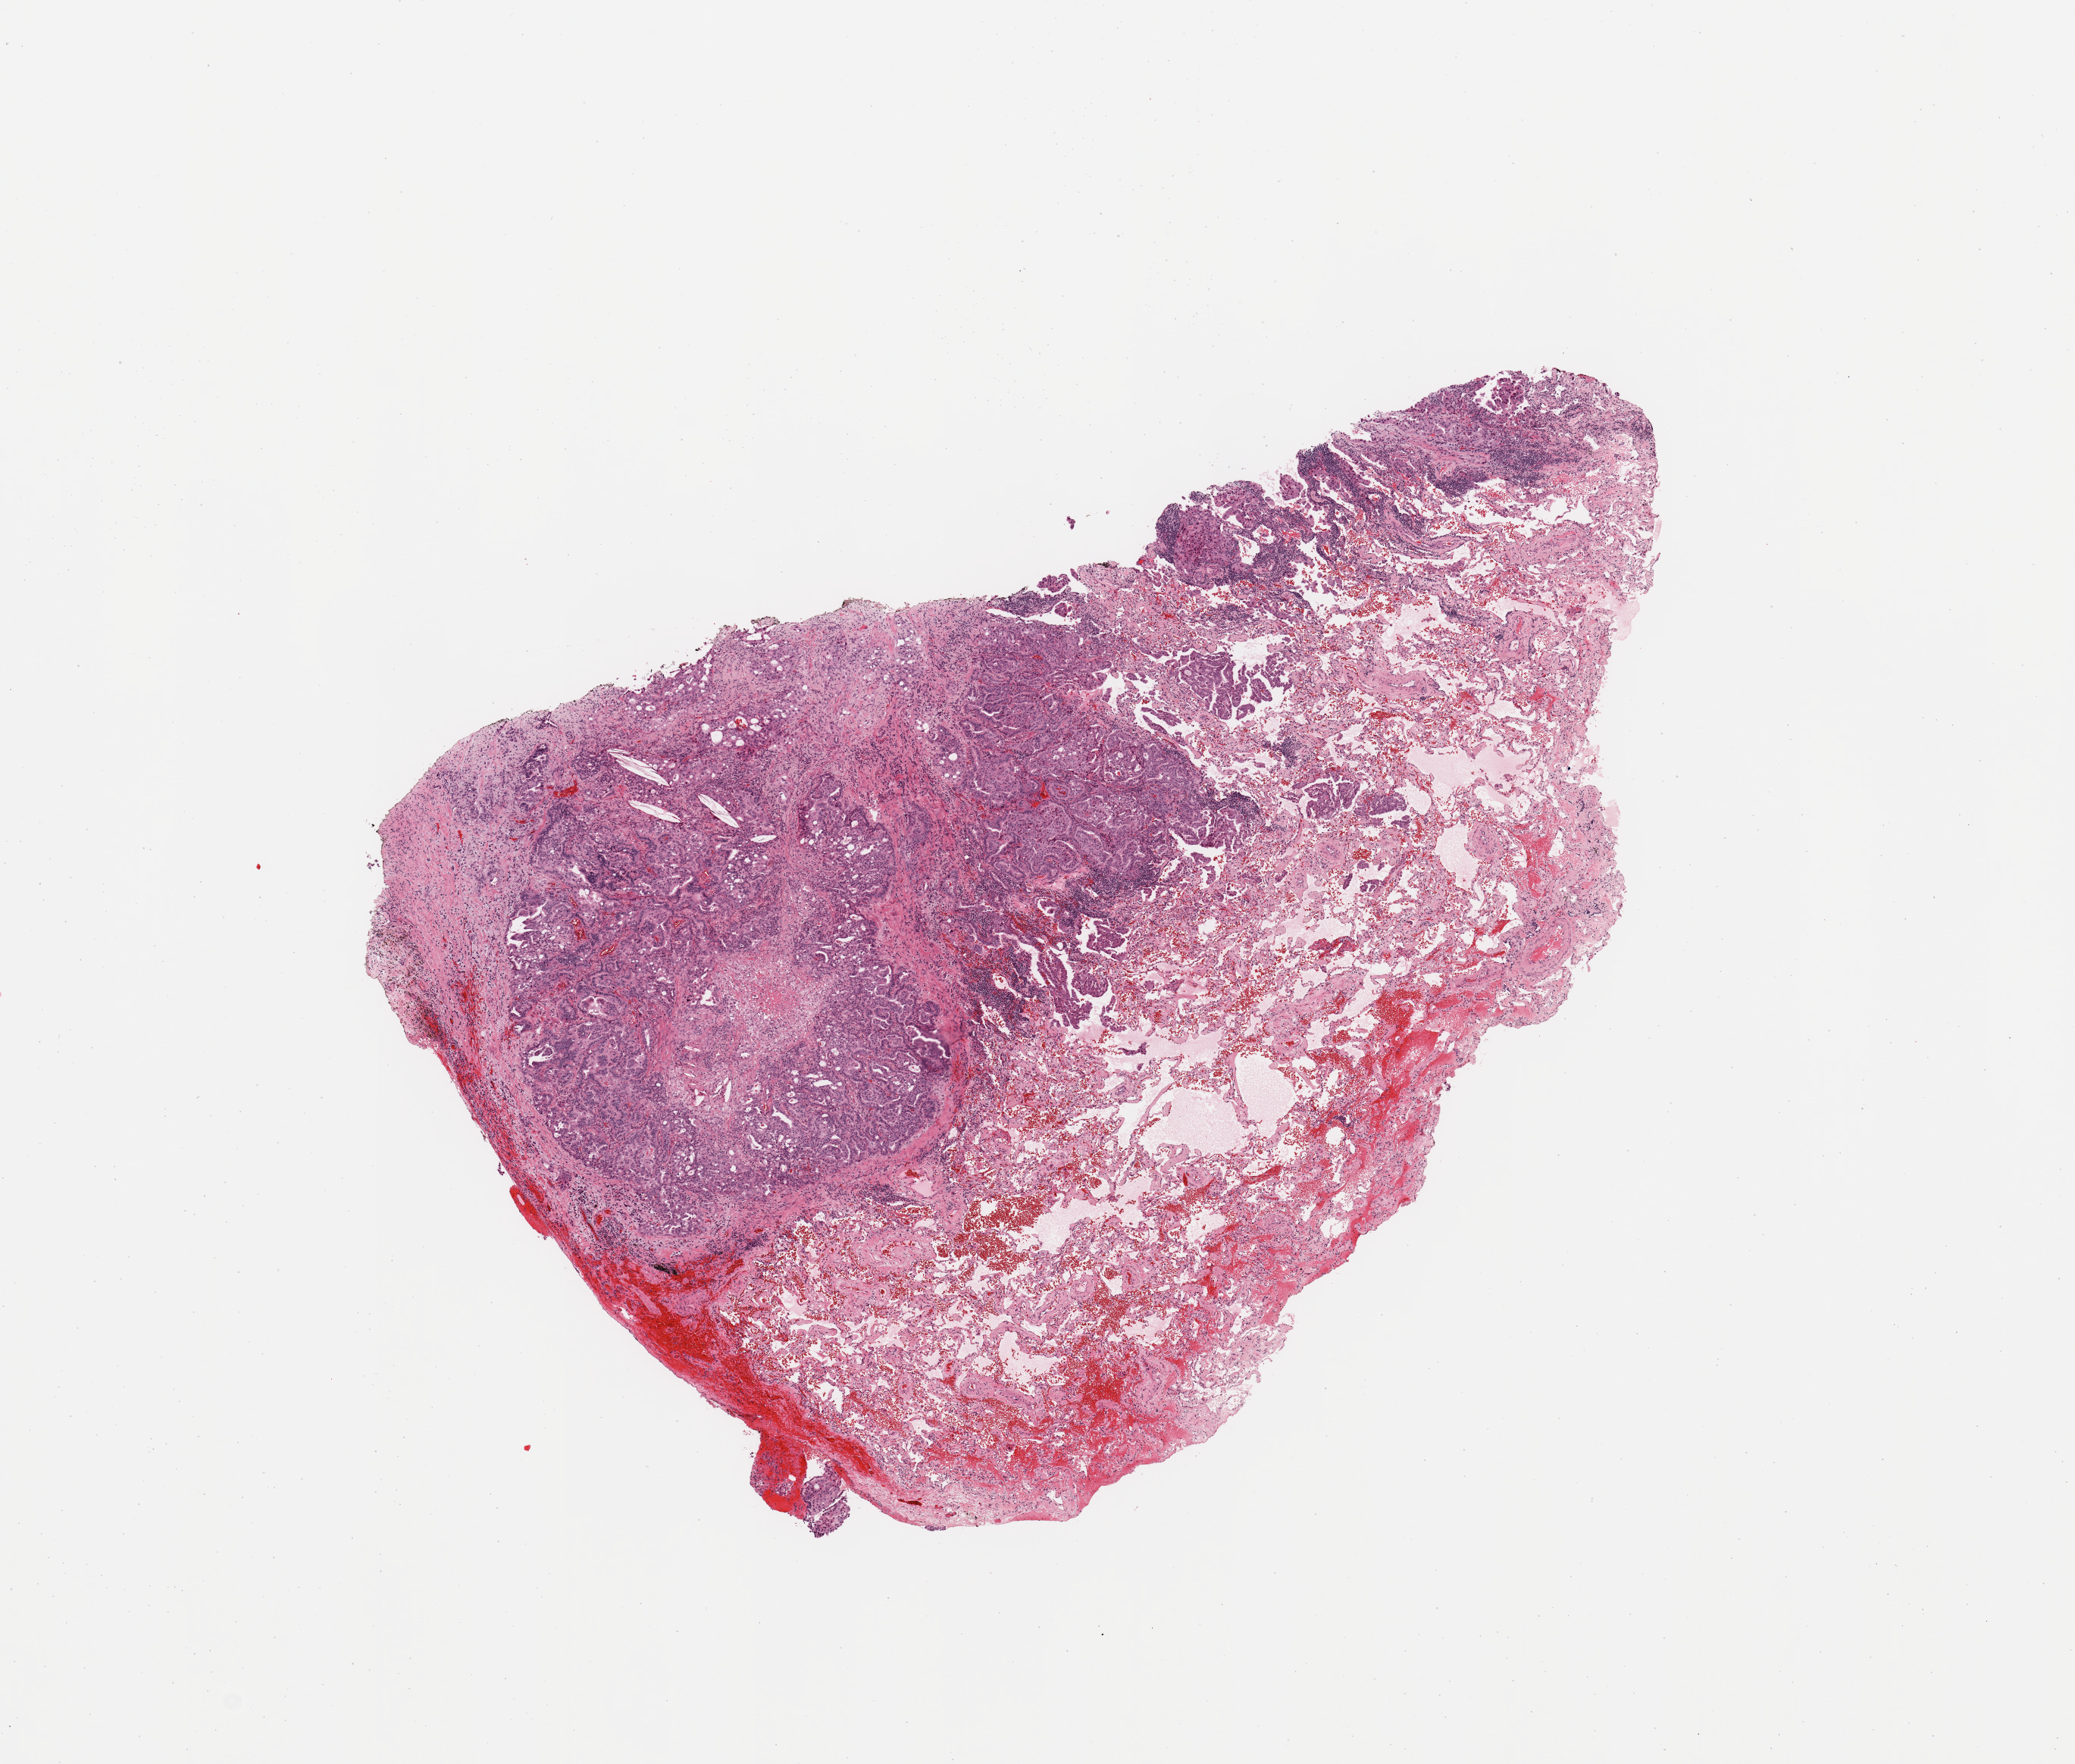
Digitized H&E-stained tissue section (whole slide), a low-resolution overview of the entire scanned area, about 10.8 x 9.2 mm; tumour tissue sample, lung. Female, 73 y/o. Histologic grade: G2 (moderately differentiated).
AJCC pathologic stage: IA. Diagnosis: Adenocarcinoma, NOS. Primary tumour site (as recorded): left upper lobe.